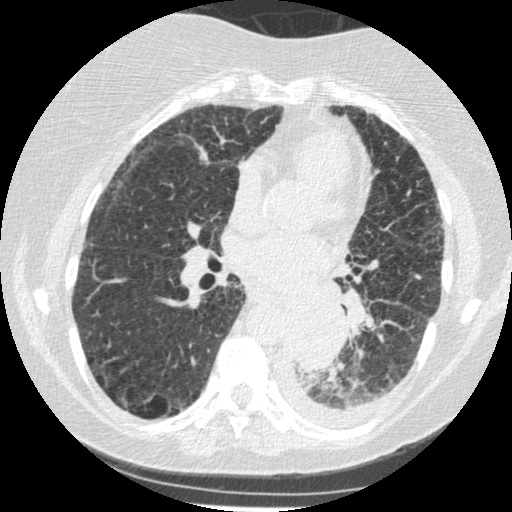
Chest CT (low-dose screening protocol), one axial image; third screening round (two years after baseline); lung window (W 1500 / L -600 HU); 1.25 mm slice thickness; 120 kVp. Female, age 60 years at enrolment. Former smoker at enrolment.
• Lesion marked by an expert reader, bounding box (x1, y1, x2, y2) in pixels: (274, 305, 343, 375).
• Reader record for this screening exam (exam-level; its link to the box is not recorded): non-calcified nodule or mass ≥4 mm, left lower lobe, 54 × 38 mm, smooth margins, soft tissue attenuation, pre-existing on the prior screen: yes; interval growth: yes.
• Official screen result: positive, other.
• Later outcome: lung cancer diagnosed 15 days after this screen — small cell carcinoma, NOS, left lower lobe, undifferentiated (G4), stage IV (AJCC 6th edition), 69 mm at pathology.